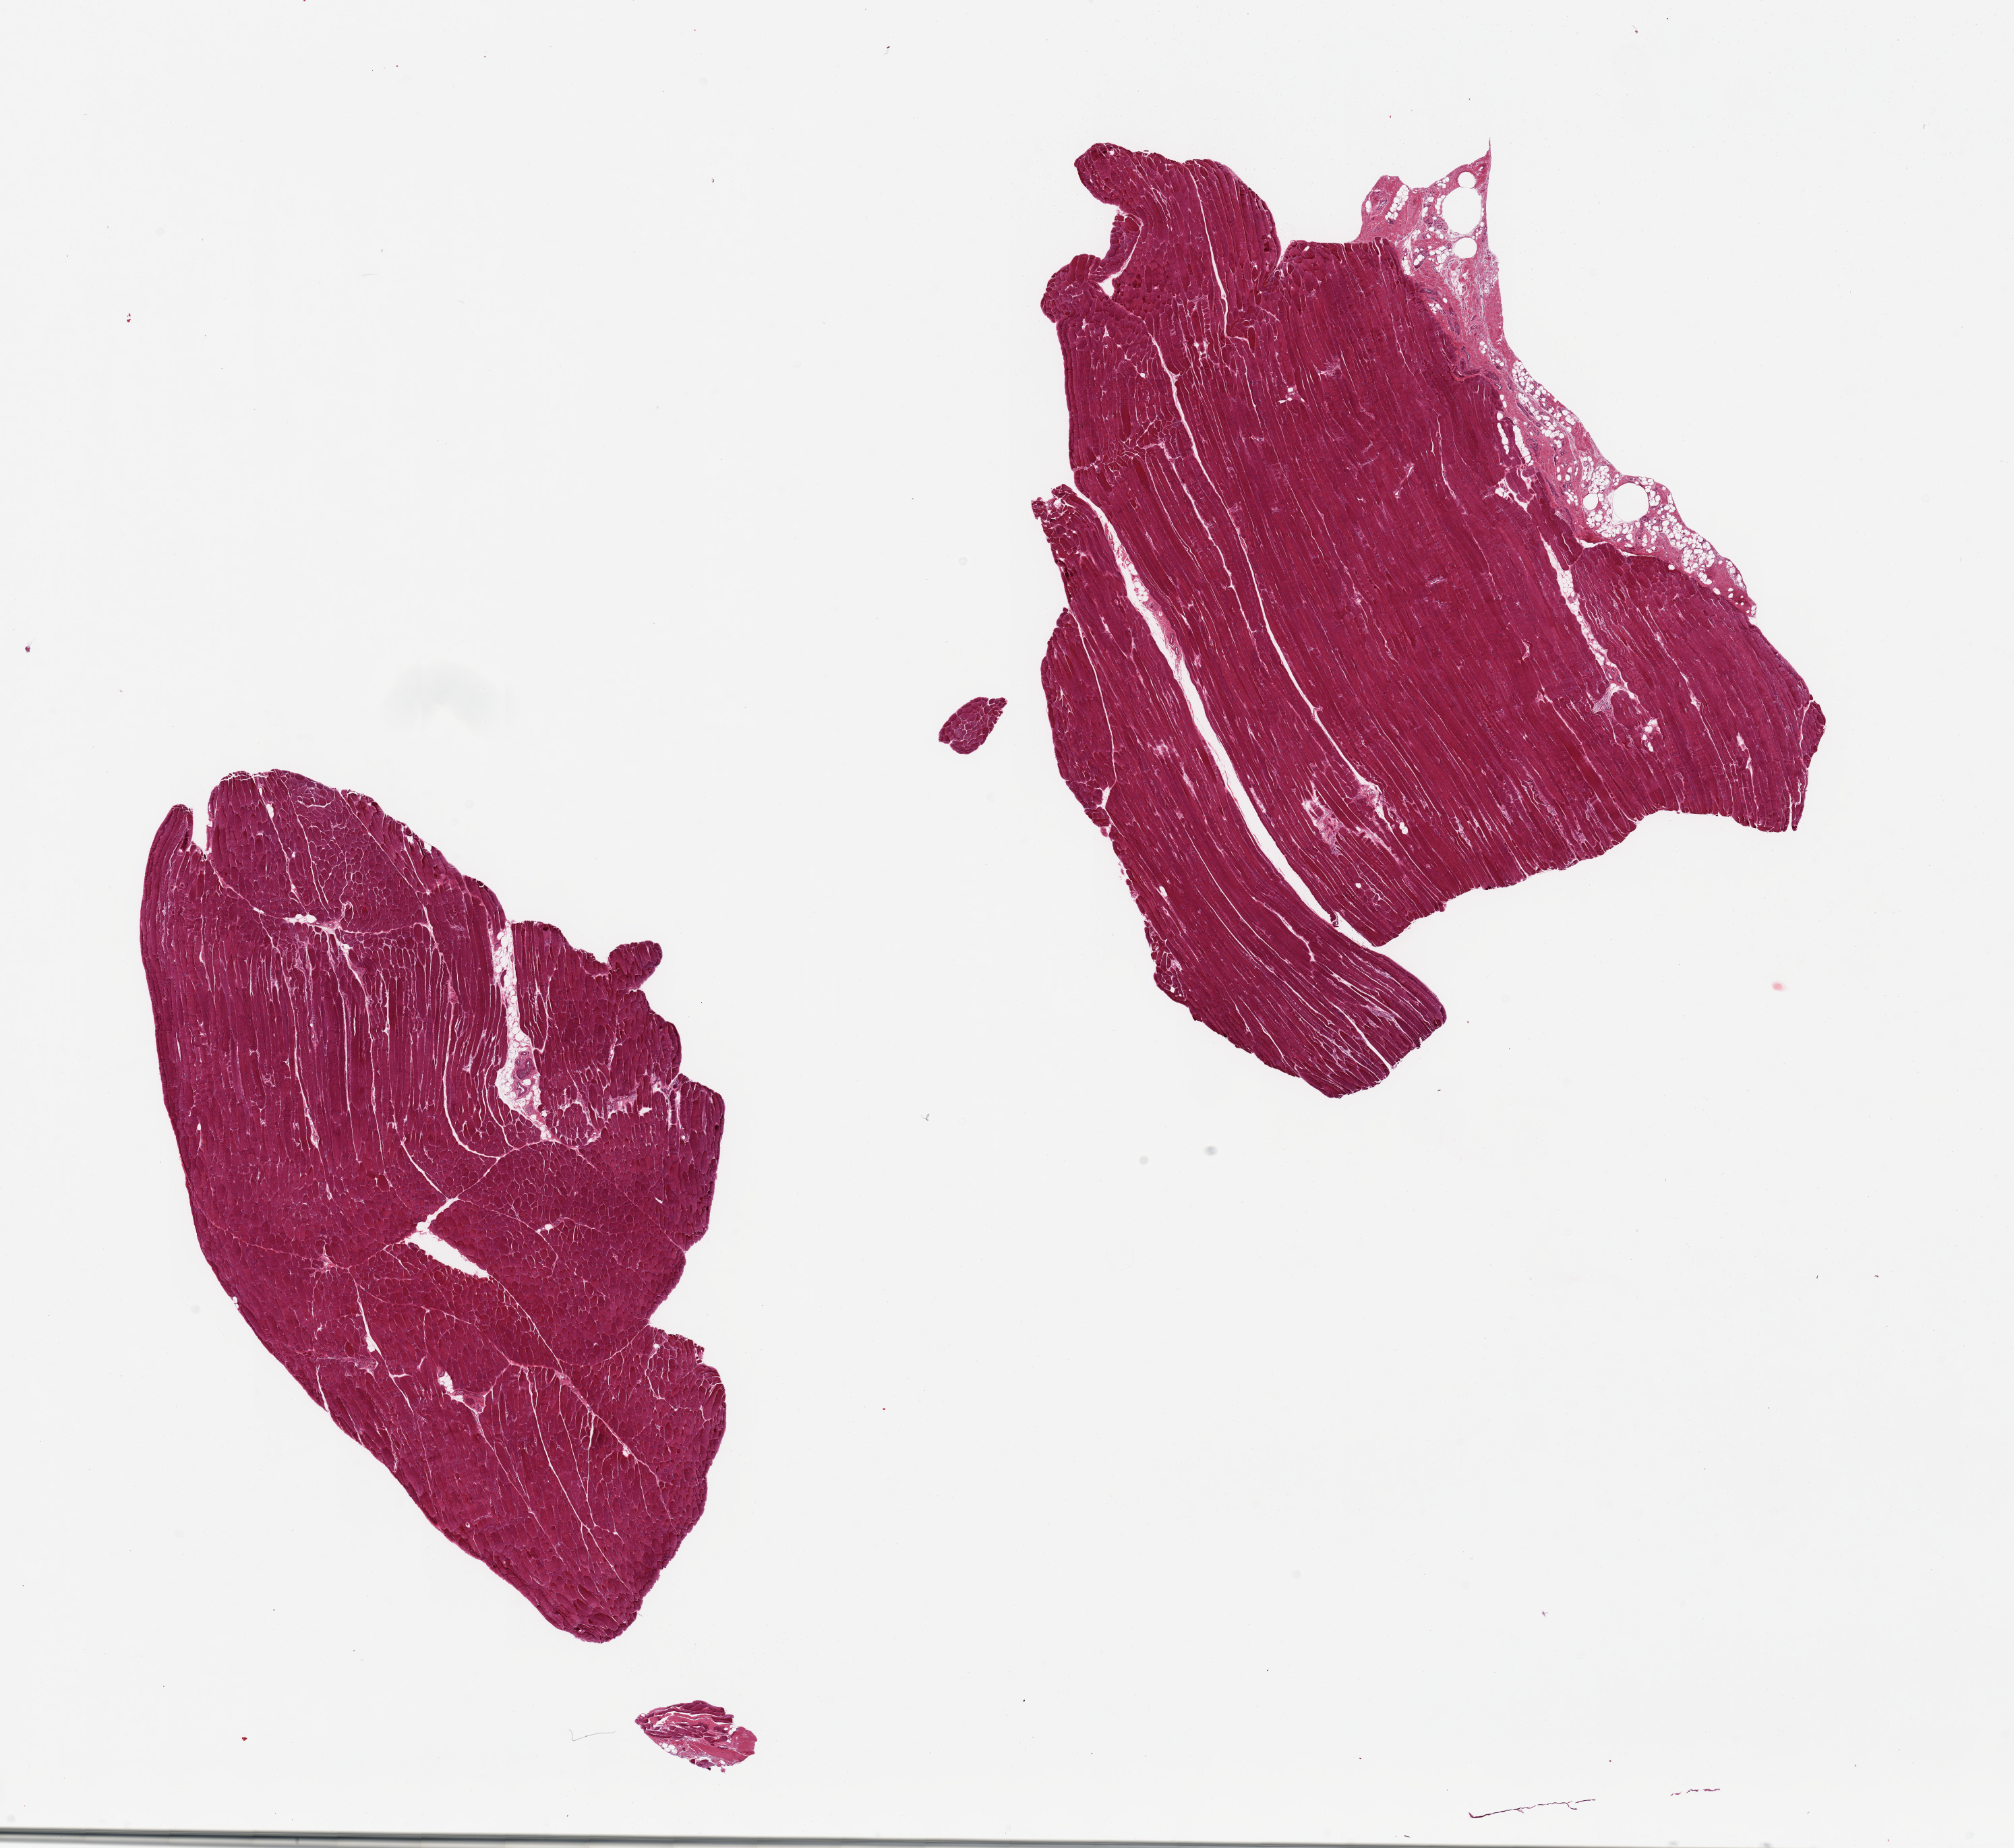
Haematoxylin and eosin whole-slide image, brightfield — low-resolution overview of the scanned area, about 23.6 x 21.7 mm, PAXgene-fixed, paraffin-embedded tissue, sampled site (target tissue): skeletal muscle, donor tissue sample. Donor: male.
Pathologist's review note for this sample: 2 pieces, %-10% adherent/interstitial fat/ fasica.